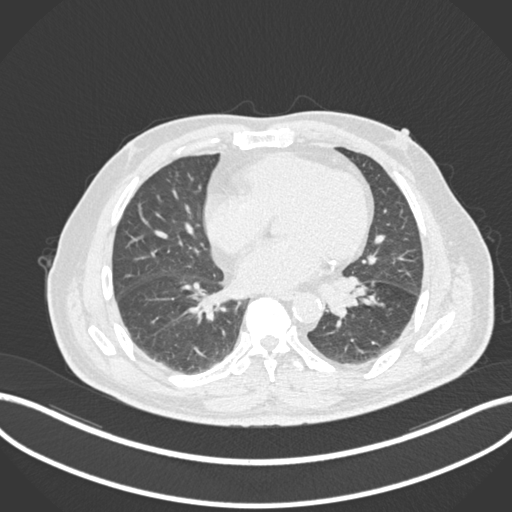
Chest CT, one axial slice; slice 50 of 161 in the series (ordered by position); reconstruction kernel B30f; 120 kVp; lung window (W 1500 / L -600 HU); 512 × 512 image matrix, field of view 400 × 400 mm. Male patient, age 71 years. From the clinical record (not read from this slice): clinical TNM (as recorded): T1b N0 M0.
Annotated regions visible in this slice (rectangle marked by the reading radiologist):
- lung tumour (recorded histology: squamous cell carcinoma): bounding box [x1, y1, x2, y2] px = [327, 272, 366, 319]